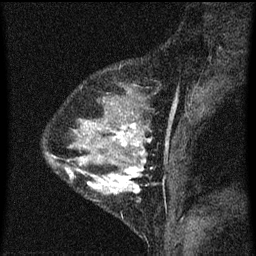
Breast MRI (dynamic contrast-enhanced), one sagittal slice. Position 22 of 60 along the scan axis. Dynamic contrast-enhanced series, image 2 of 3 at this slice position (ordered by acquisition). 1.5 T. TE 4.2 ms, TR 8 ms. 256 × 256 image matrix, field of view 180 × 180 mm. Female patient, age 33 years.
Outlined on this slice (semi-automatically segmented with operator editing):
- analysis volume of interest (the breast-tissue region the enhancement analysis was run in; not a lesion): bounding box <67,118,152,213> (left, top, right, bottom; pixels)
- tumour enhancement mask (voxels above the 70 % enhancement threshold inside the analysis volume of interest): <87,124,152,195>